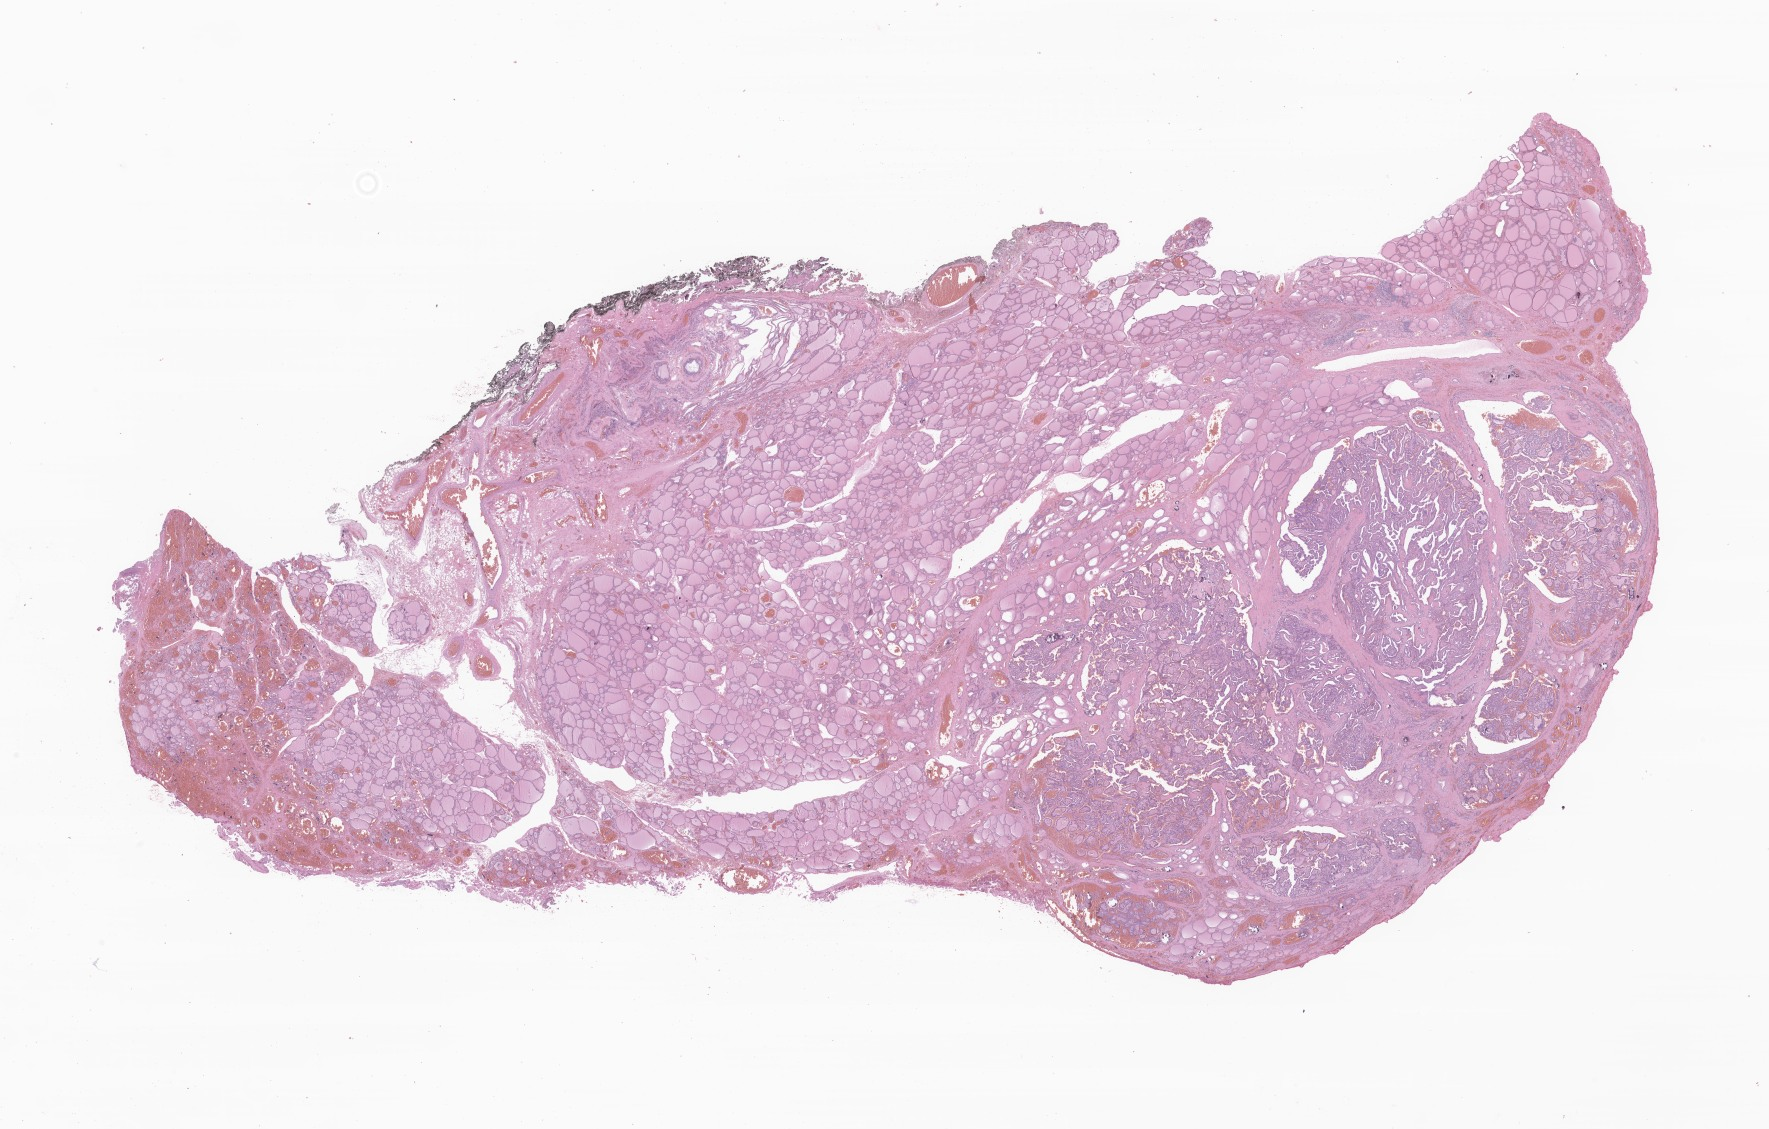
Hematoxylin and eosin (H&E) whole-slide image of tumor tissue from the thyroid, low-resolution overview of the scanned area, about 29.8 x 19.0 mm; FFPE section. Female patient, age 174 months (14 years 6 months).
Diagnosis (ICD-O-3 morphology term): Papillary adenocarcinoma, NOS.